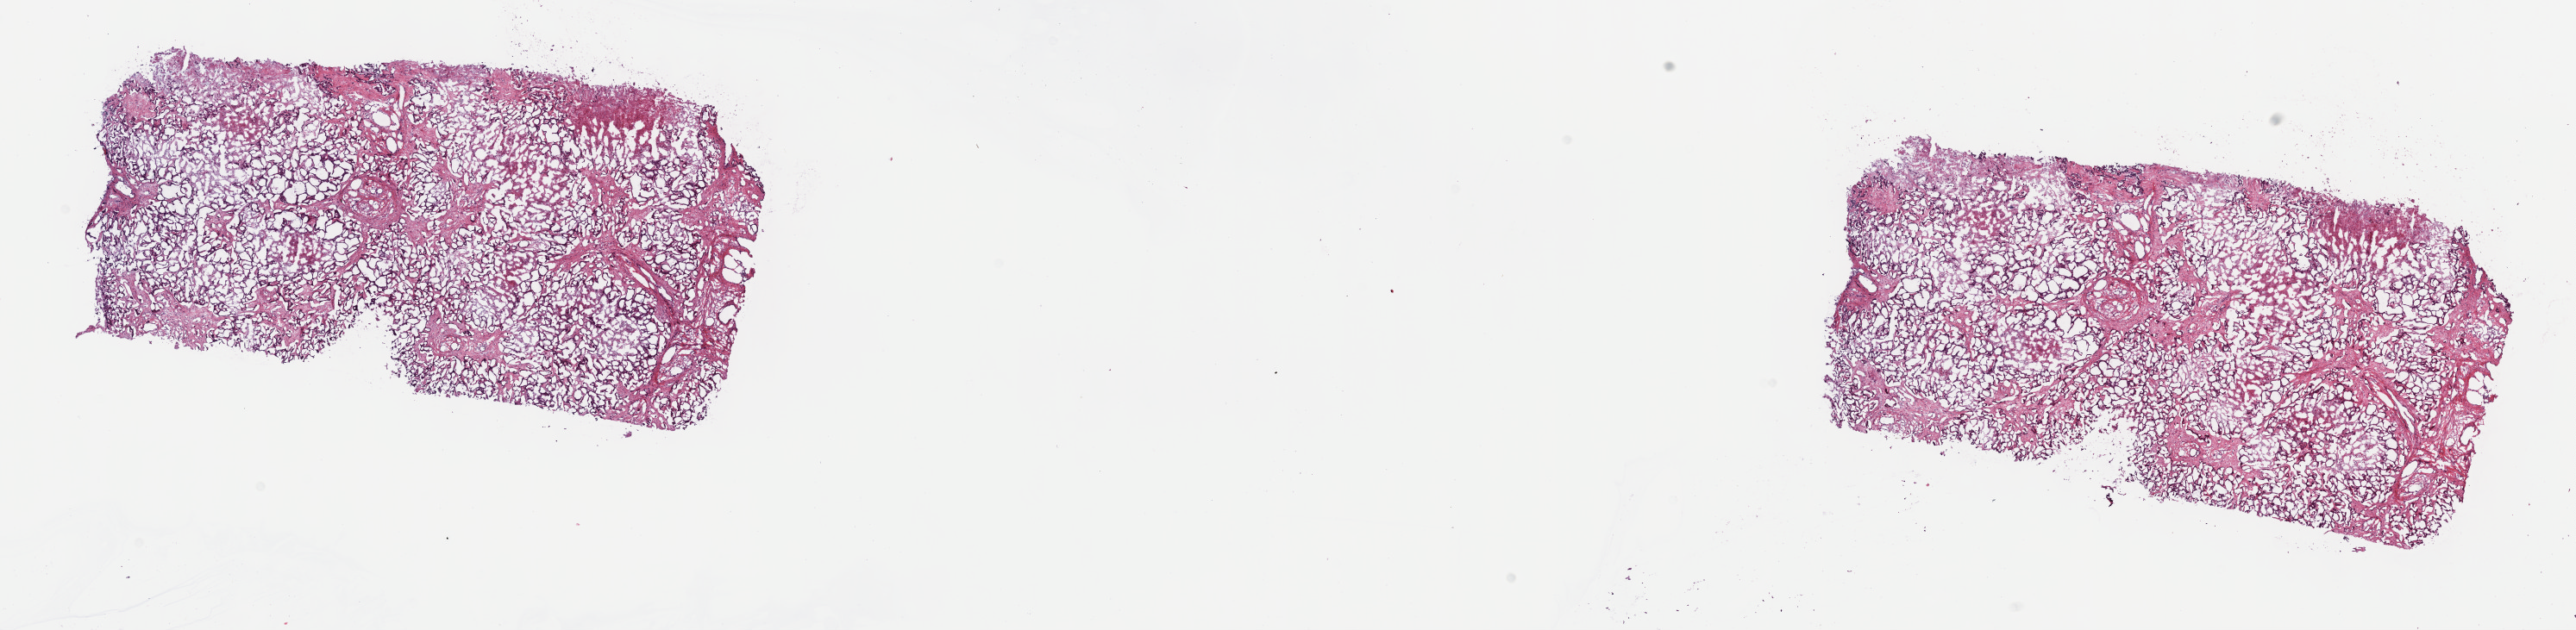
H&E whole-slide image, a low-resolution overview of the entire scanned area, about 24.2 x 5.9 mm (from a 40x scan), frozen section from the top of the tissue portion, sample: primary tumour, bile duct. Female, age 75 years at initial diagnosis. Histologic grade: G3 (poorly differentiated). Pathologist review of this section (percent, as recorded): tumour cells 90%, tumour nuclei 65%, normal cells 0%, stromal cells 0%, necrosis 10%. Inflammatory infiltration, as recorded: lymphocyte infiltration 2%, monocyte infiltration 0%, neutrophil infiltration 0%.
- AJCC pathologic stage: I (7th edition)
- diagnosis: Cholangiocarcinoma